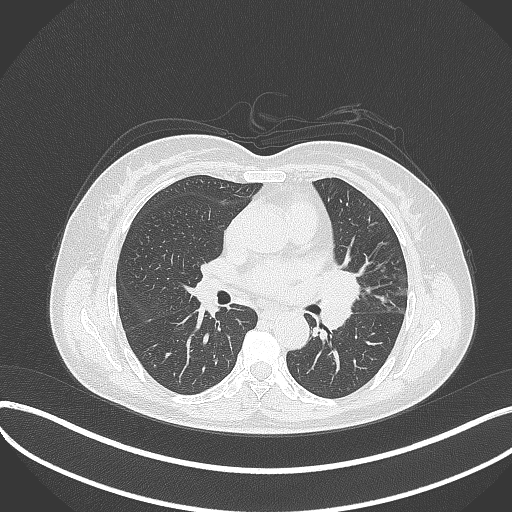
Chest CT, one axial slice; slice 189 of 373 in the series (ordered by position); reconstruction kernel B70f; lung window (W 1500 / L -600 HU); 1 mm slice thickness; 512 × 512 image matrix, field of view 400 × 400 mm. Patient: female, 54 years. From the clinical record (not read from this slice): clinical TNM (as recorded): T2a N1 M0.
Annotated regions visible in this slice (rectangle marked by the reading radiologist):
- lung tumour (recorded histology: small cell carcinoma): bounding box [x1, y1, x2, y2] px = [322, 264, 364, 333]